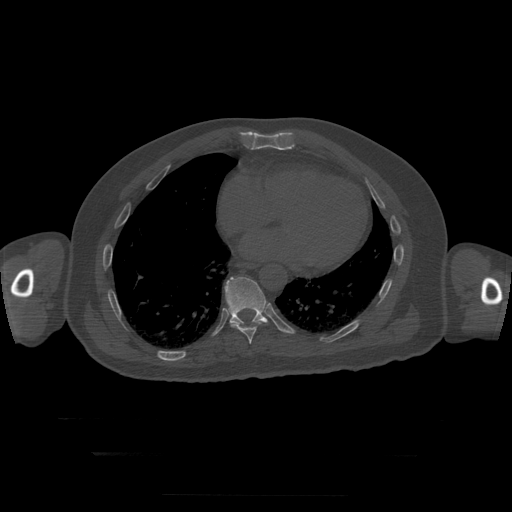
CT including the spine, one axial slice; position 135 of 397 along the scan axis; reconstruction kernel STANDARD; 120 kVp; bone window (W 1800 / L 400 HU); 1.25 mm slice thickness; 512 × 512 image matrix, field of view 510 × 510 mm. Patient age 73 years. Case-level facts recorded for this patient, not image findings: primary cancer: prostate.
Outlined on this slice (semi-automatic segmentation, software-assisted and operator-edited):
- T10 vertebra: bounding box [x1, y1, x2, y2] px = [225, 277, 268, 326]
- T9 vertebra: [231, 319, 267, 344]